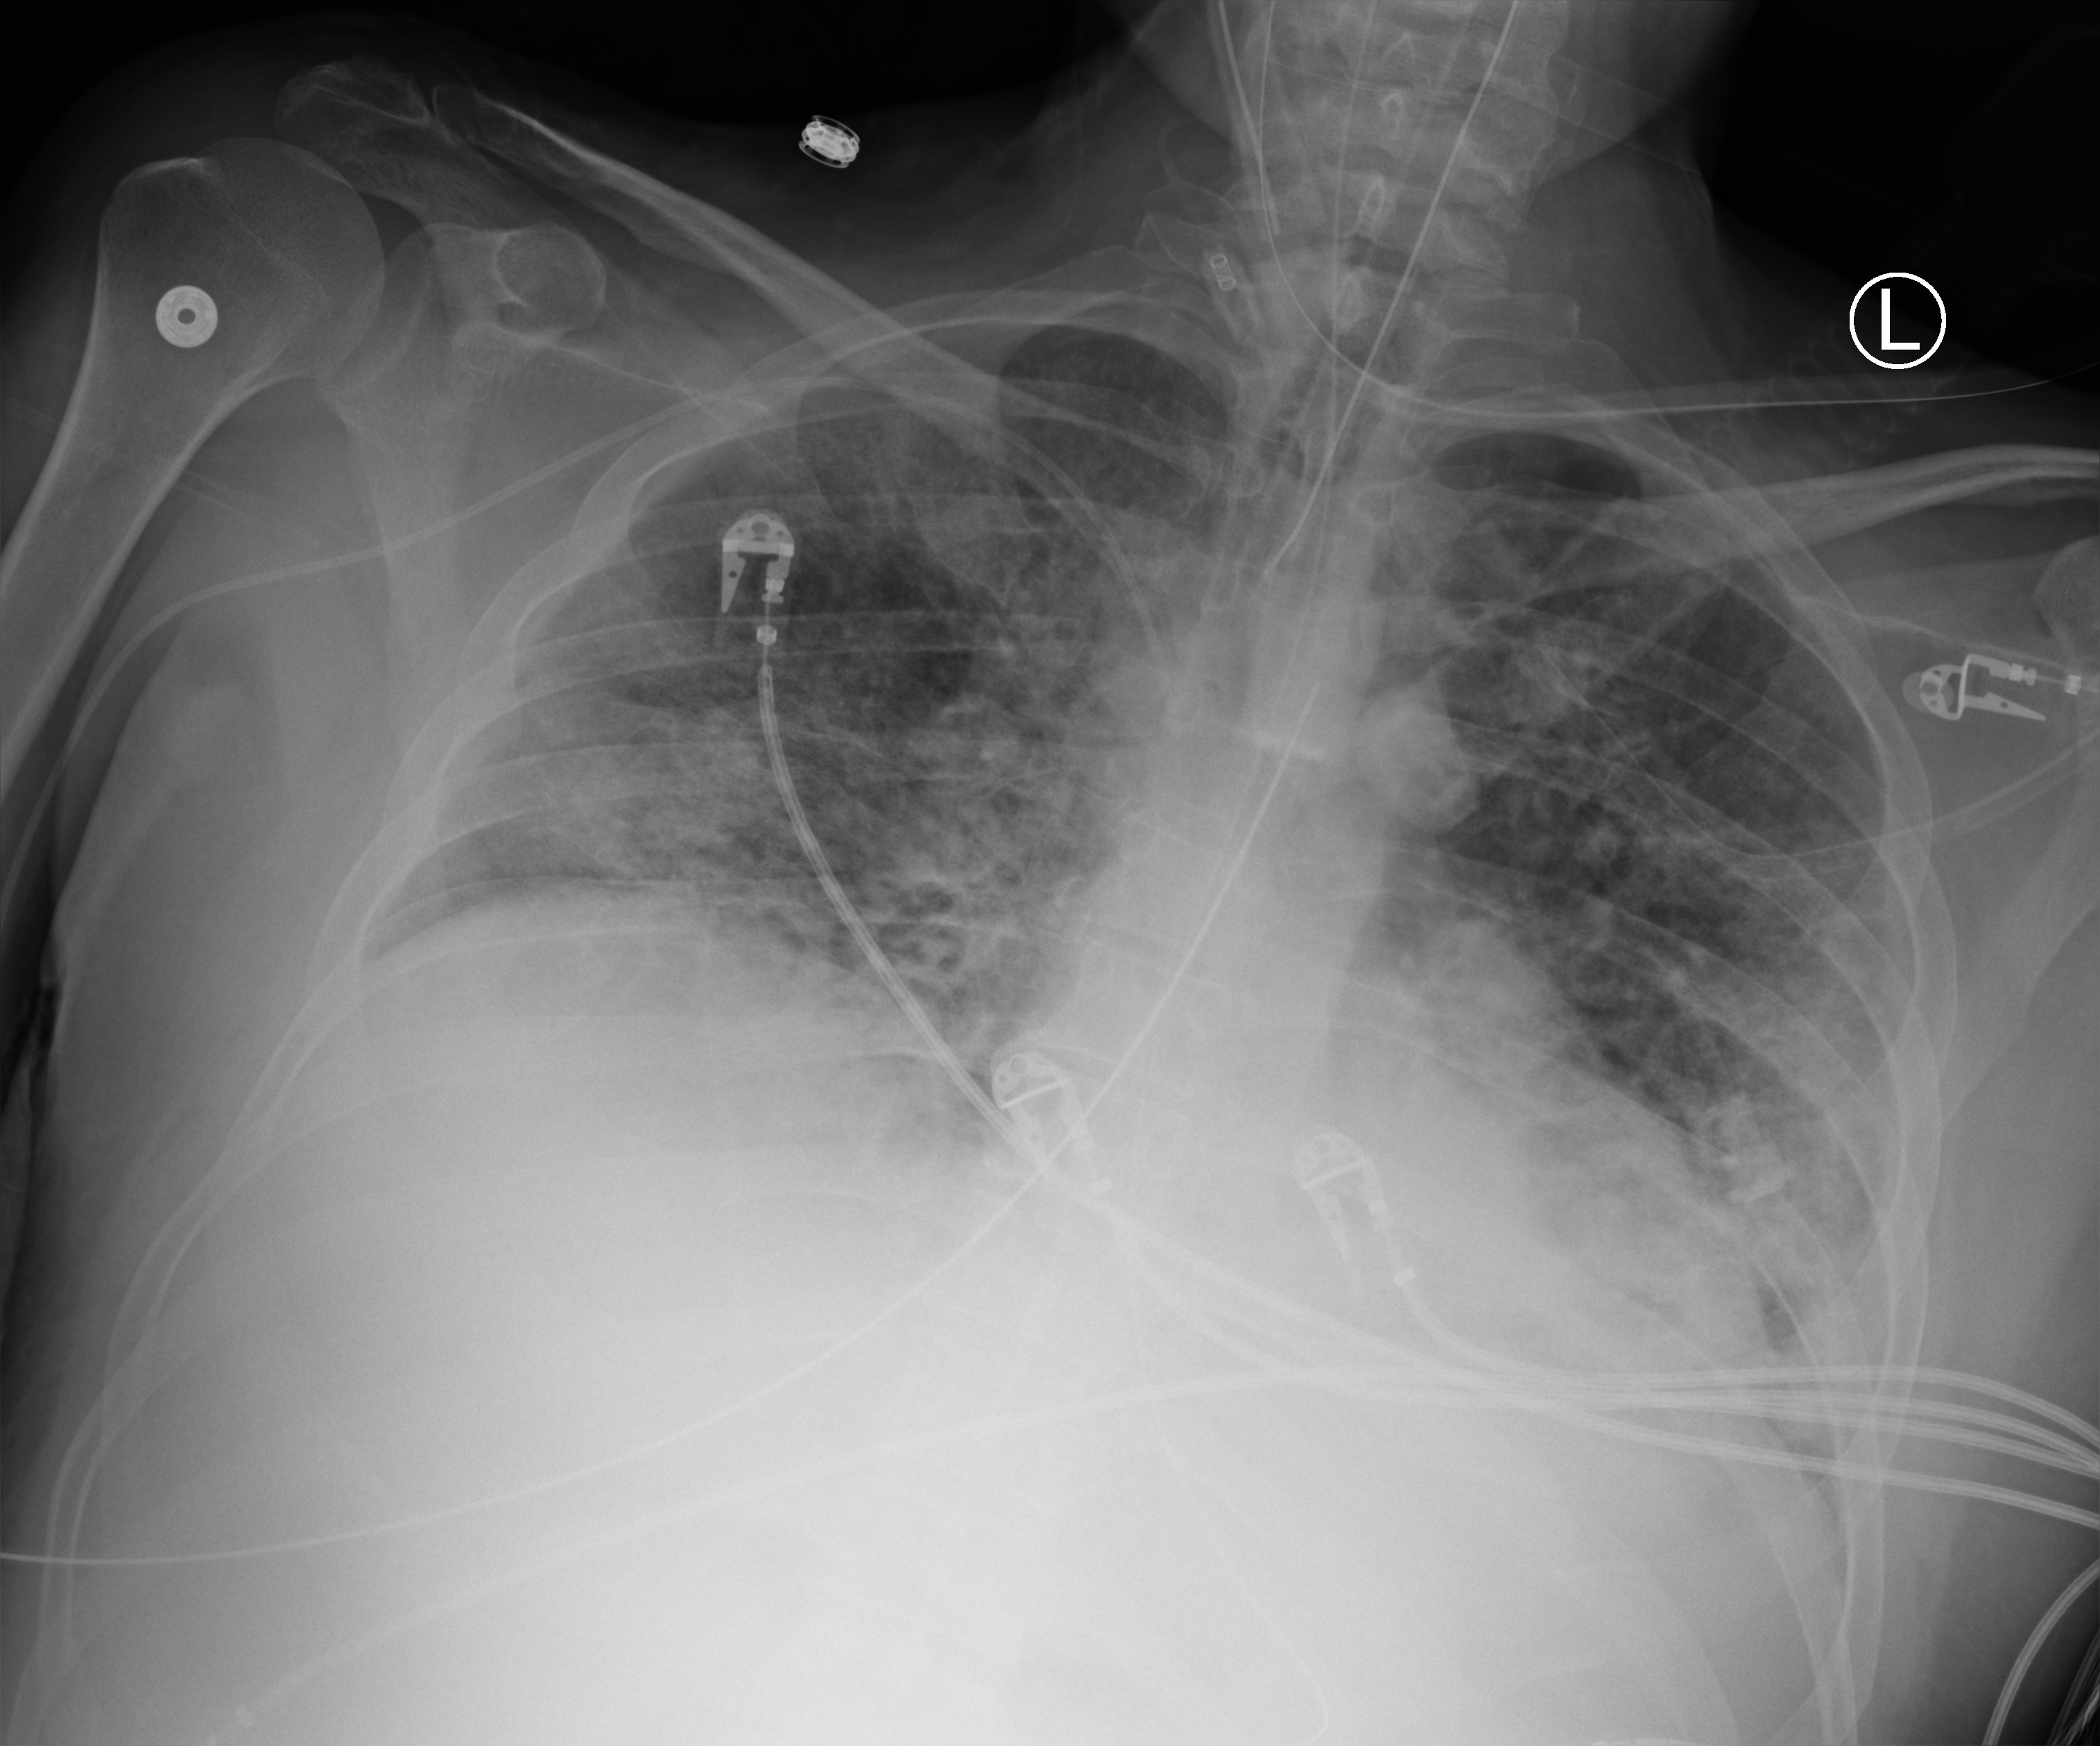
Portable chest radiograph, anteroposterior (AP) projection. Male patient hospitalised with COVID-19, age 18–59 years.
Admission-level facts for this patient (not findings on this image; timing relative to this image not recorded): length of hospital stay: 48 days; admitted to intensive care during this hospital stay: yes.